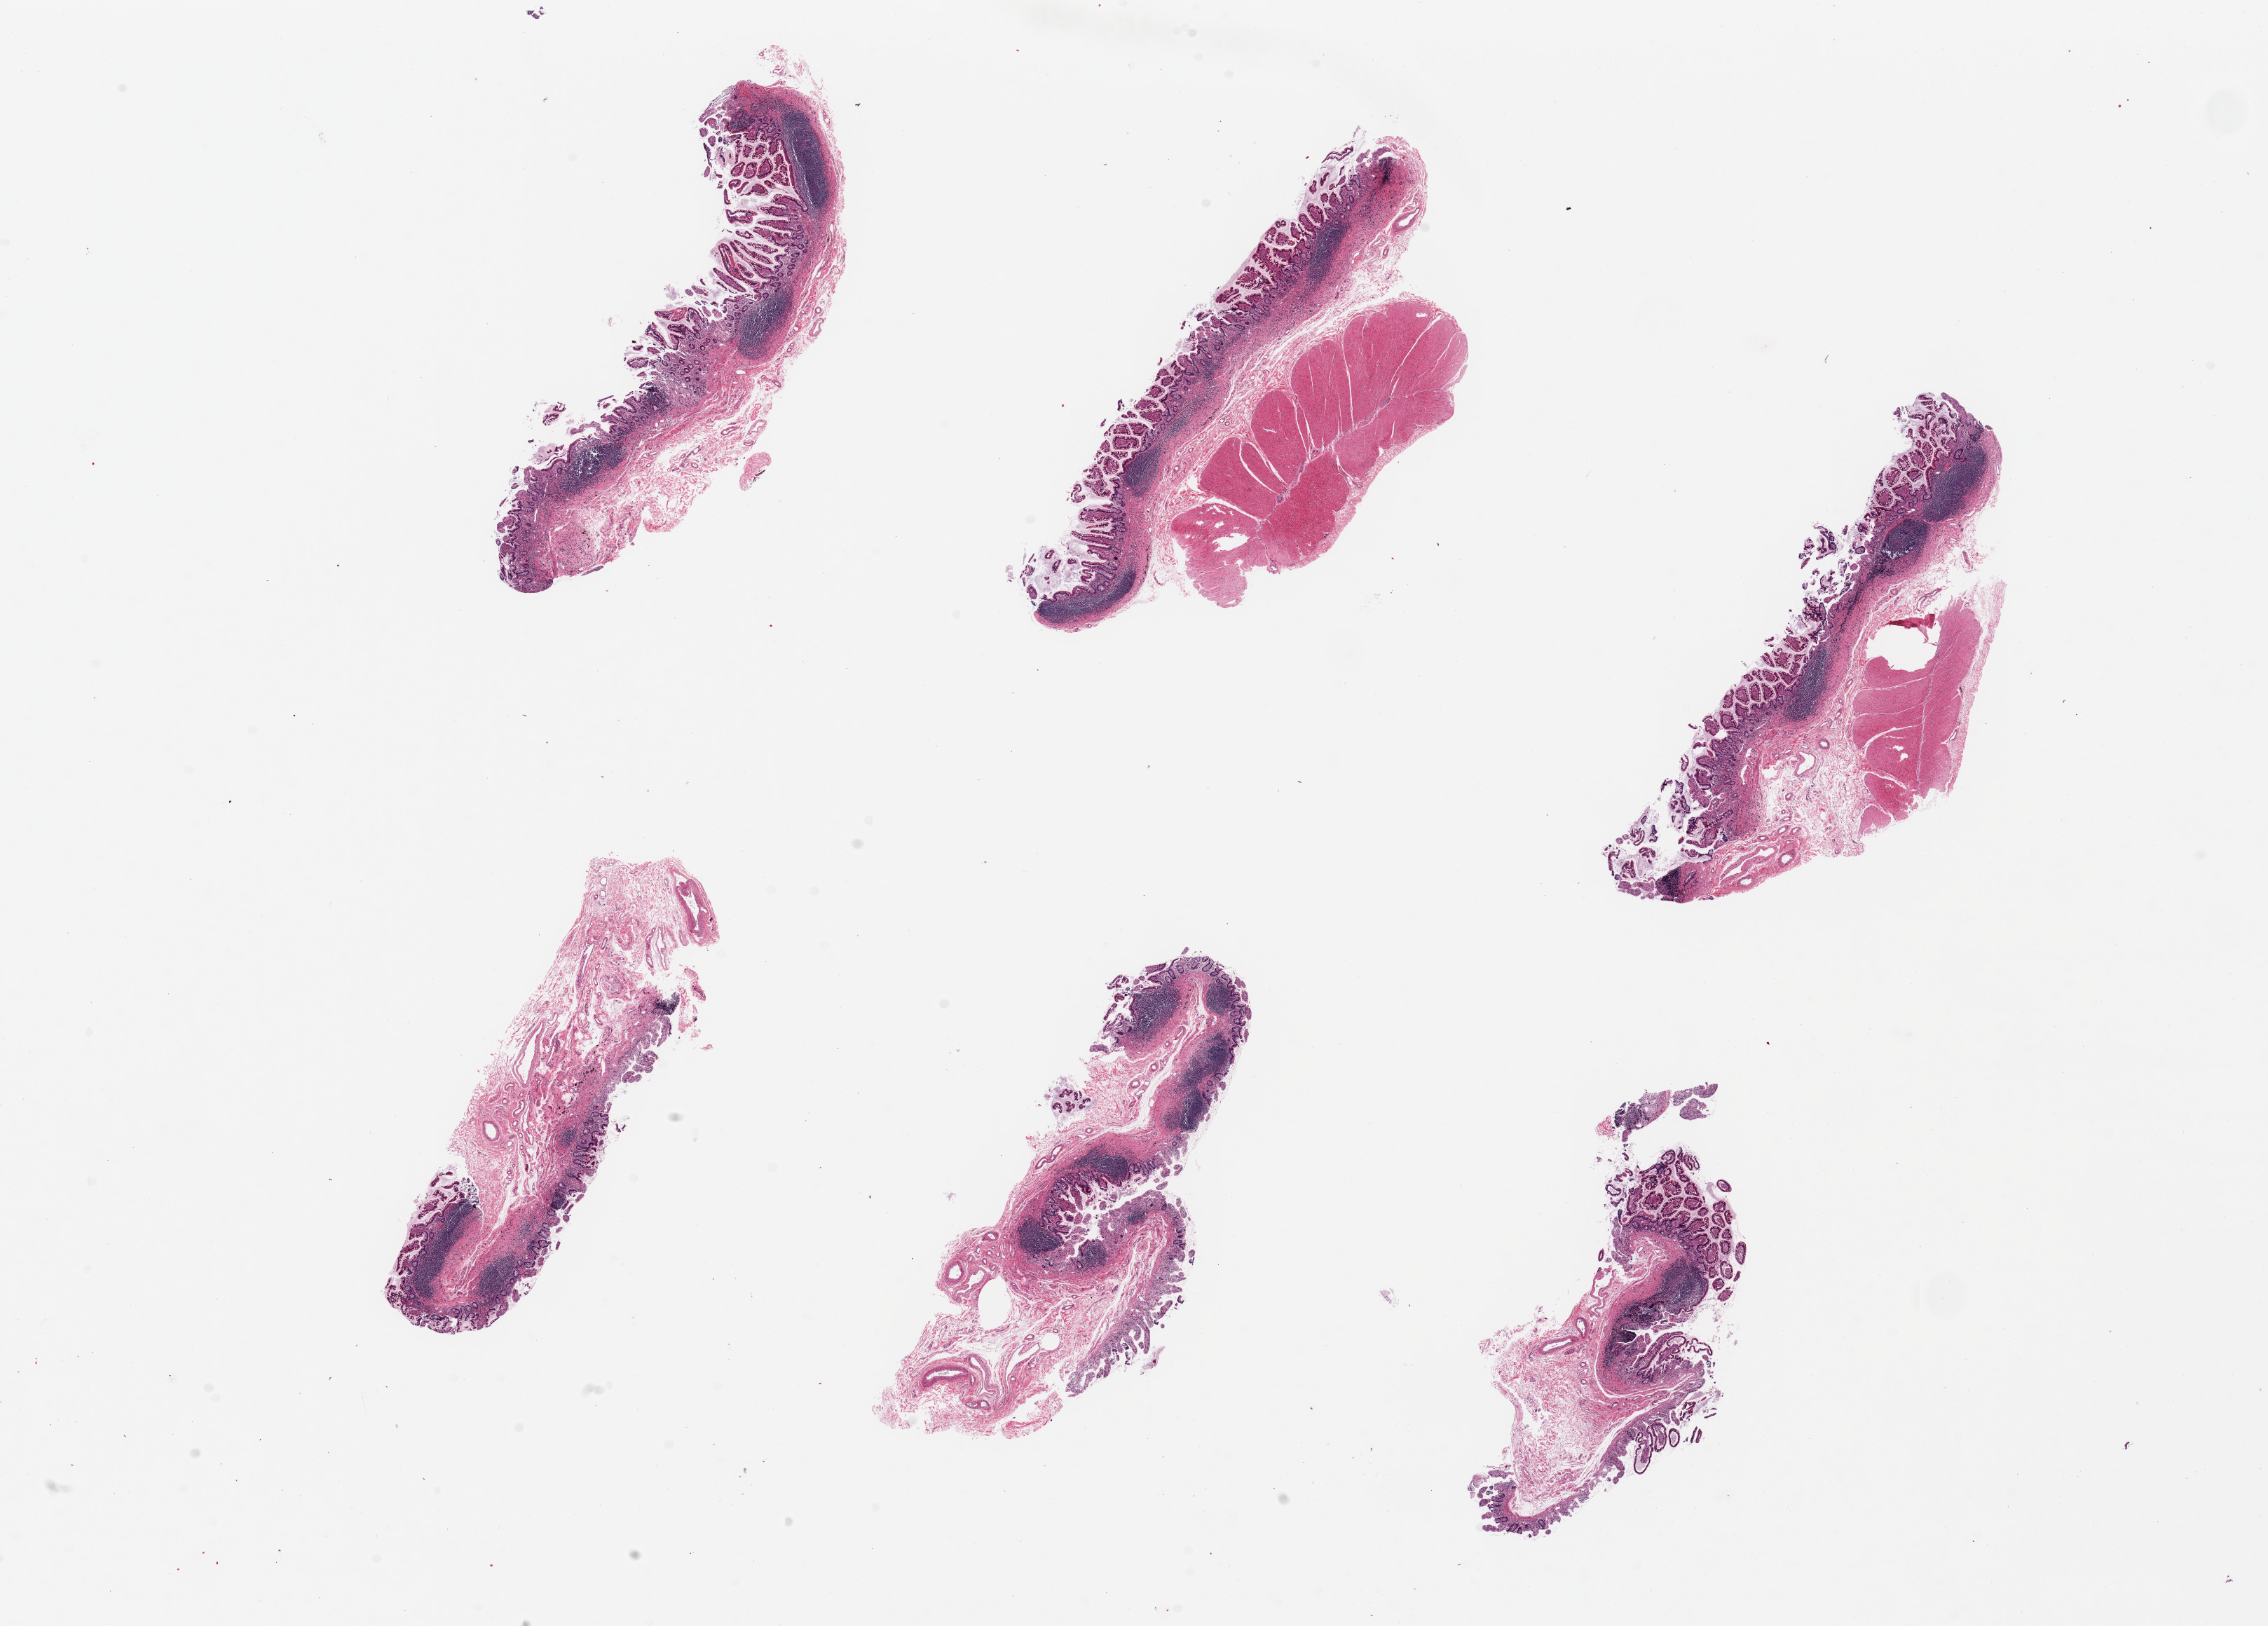
Digitized haematoxylin and eosin-stained section — shown as a low-resolution overview of the whole scanned area (about 25.6 x 18.4 mm), PAXgene-fixed, paraffin-embedded tissue, target tissue: ileum, tissue donor sample.
Reviewer comment on this tissue sample: 6 pieces, up to 7x3mm; good specimens; 10 % lymphoid elements present.